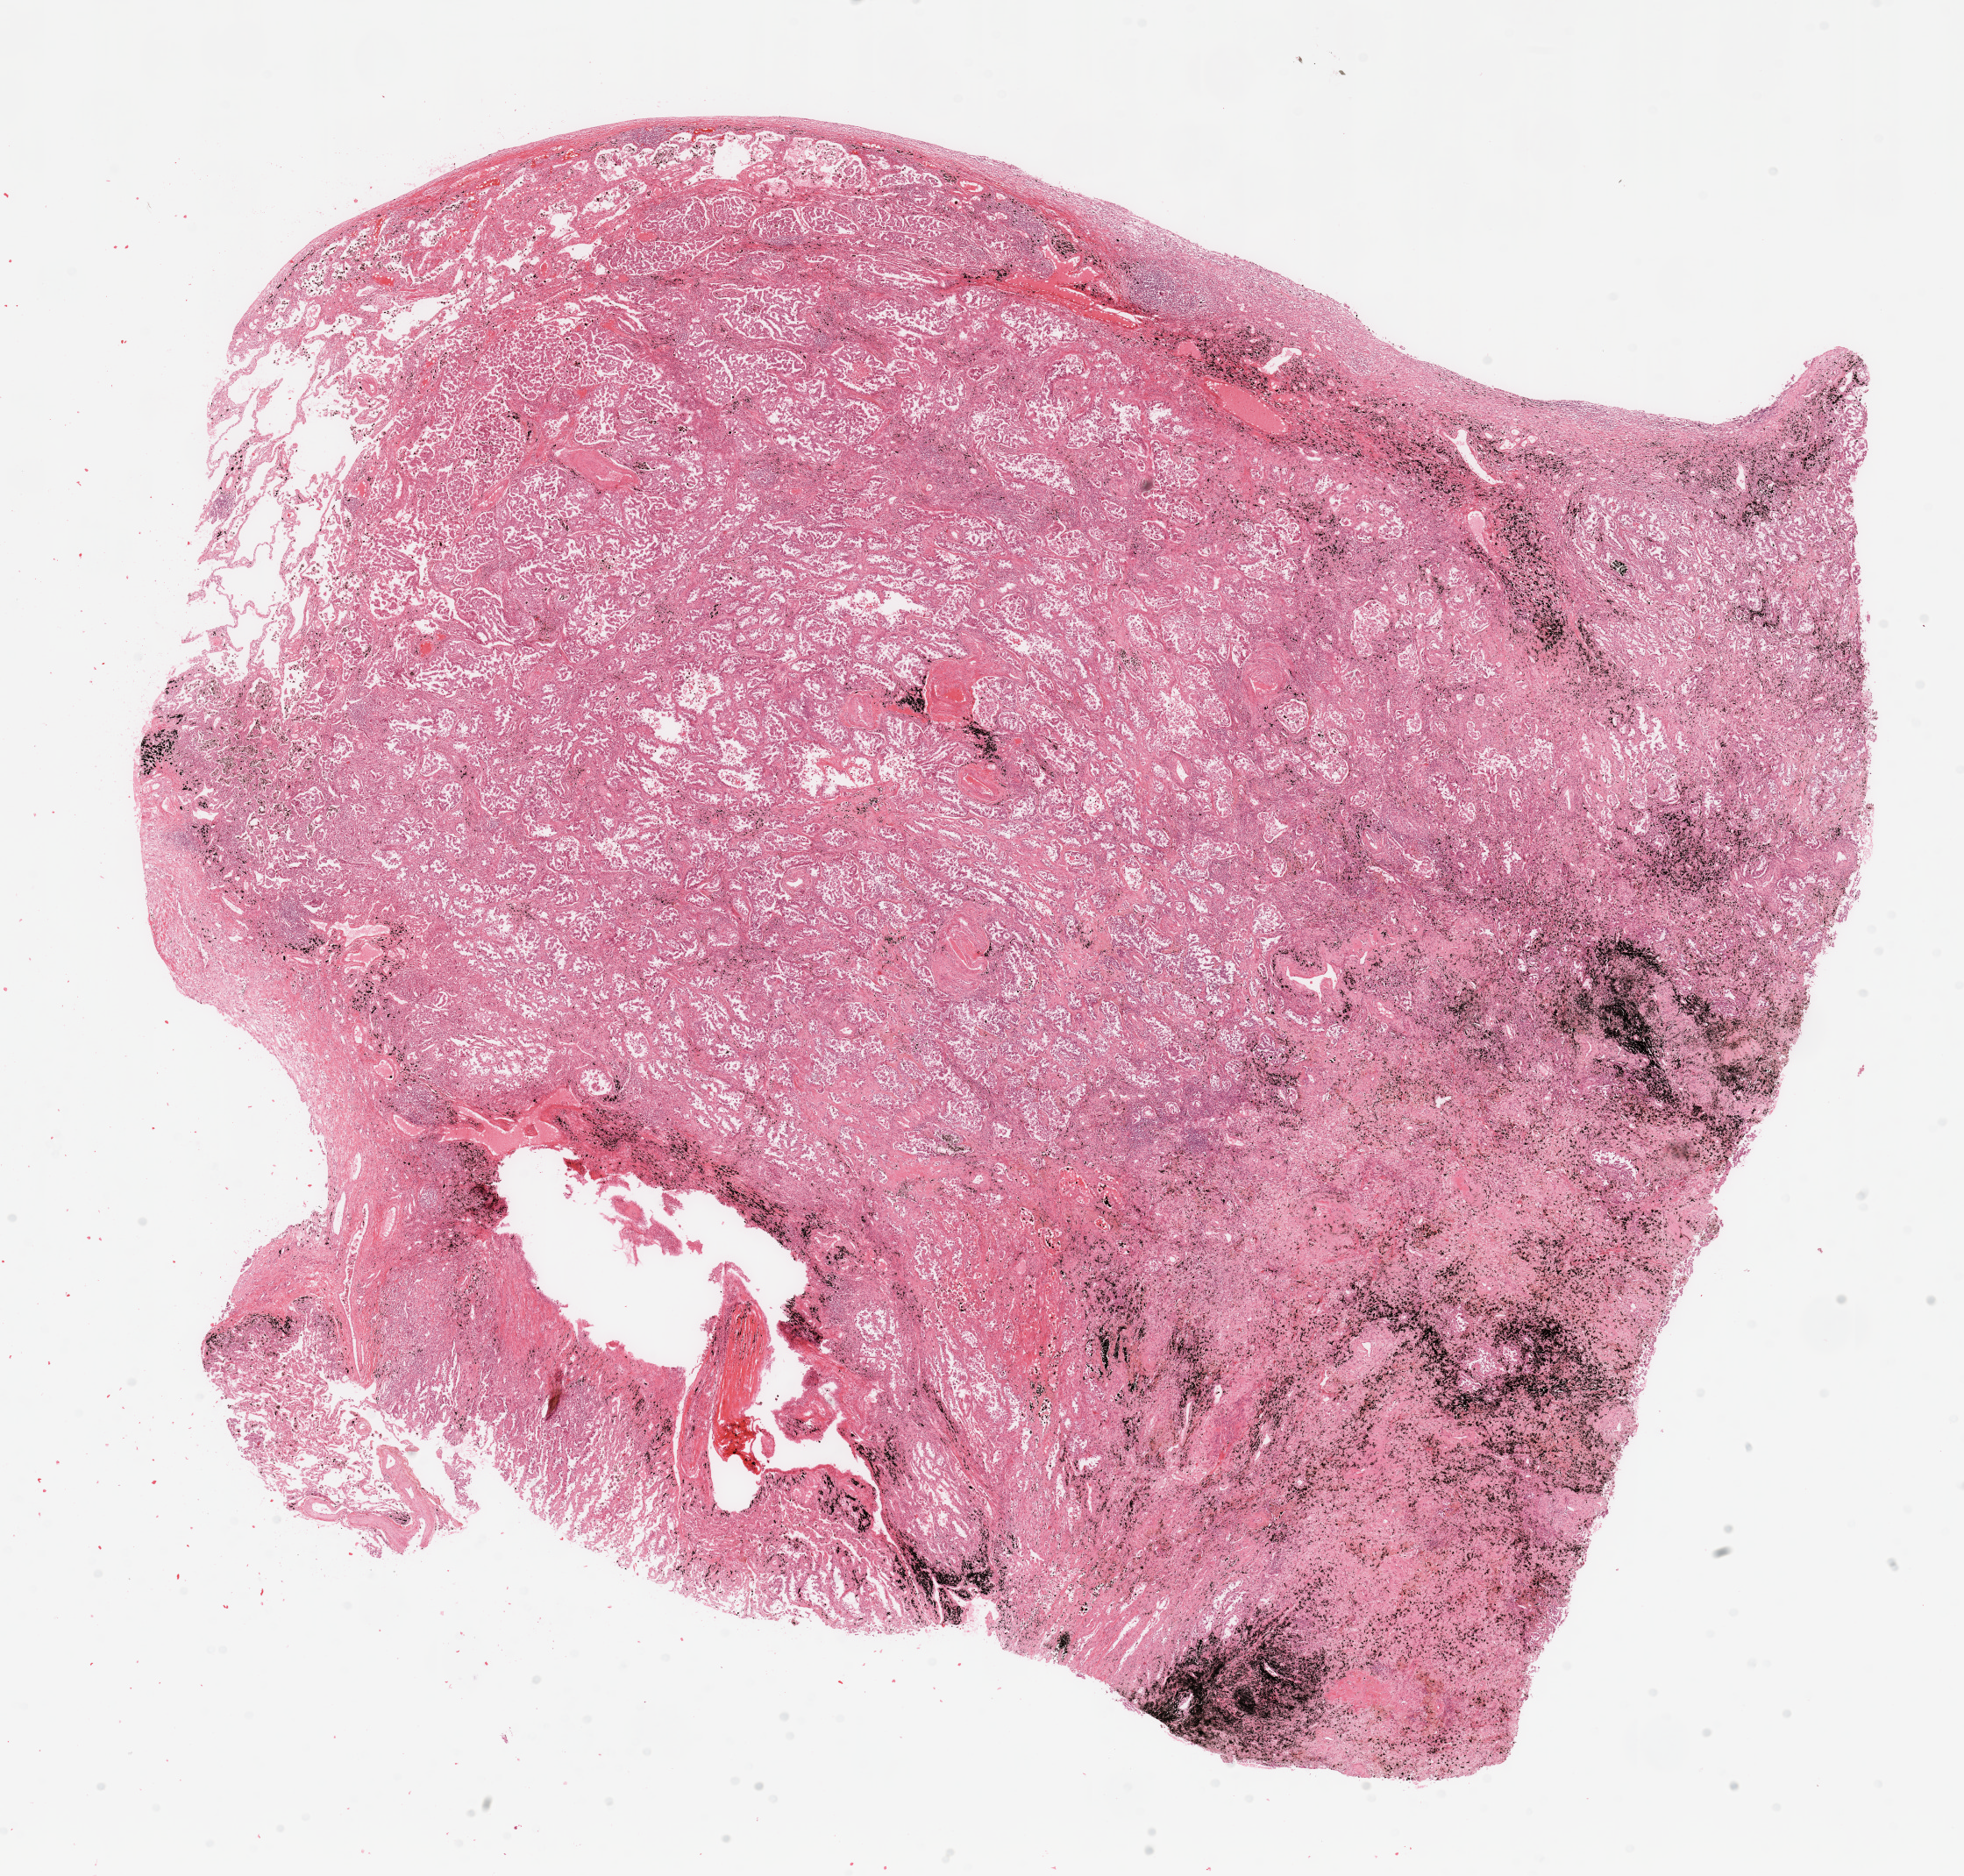
Hematoxylin and eosin (H&E) stained whole-slide image, whole scanned area (about 17.7 x 16.9 mm) shown as a low-resolution overview. Tumour tissue sample, lung. Patient: male, age 72 years. Histologic grade: G2 (moderately differentiated).
AJCC pathologic stage: IB. Histologic diagnosis: Adenocarcinoma, NOS.